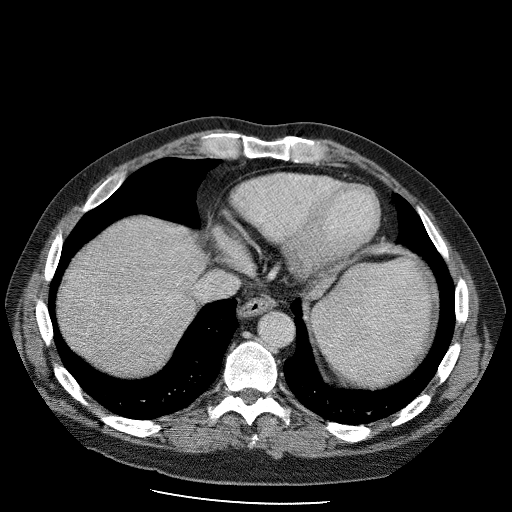
Contrast-enhanced abdominal CT (liver protocol), one axial slice; position 91 of 98 along the scan axis; 120 kVp; soft-tissue window (W 400 / L 40 HU); 2.5 mm slice thickness; 512 × 512 image matrix, field of view 400 × 400 mm. From the clinical record (not read from this slice): diagnosis: hepatocellular carcinoma (patient treated with transarterial chemoembolisation; whether this scan precedes or follows treatment is not stated here); TNM stage (as recorded): Stage-II.
Outlined on this slice (semi-automatically segmented with operator editing):
- liver parenchyma outside the tumour (the mass and vessels are separate outlines, so this box may not span the whole liver): bounding box (x1, y1, x2, y2) in pixels: (60, 214, 204, 370)